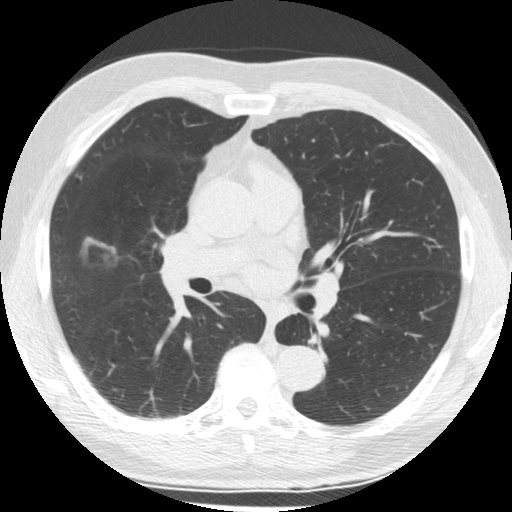
Low-dose screening chest CT, one axial slice. Slice 103 of 176 in the series (ordered by position). Reconstruction kernel STANDARD. 120 kVp. Lung window (W 1500 / L -600 HU). 2.5 mm slice thickness. 512 × 512 image matrix, field of view 348 × 348 mm.
Annotated regions visible in this slice (outlined manually by an expert reader):
- lesion 1 (tumor, middle lobe of right lung): bounding box (x1, y1, x2, y2) in pixels: (84, 237, 116, 254)